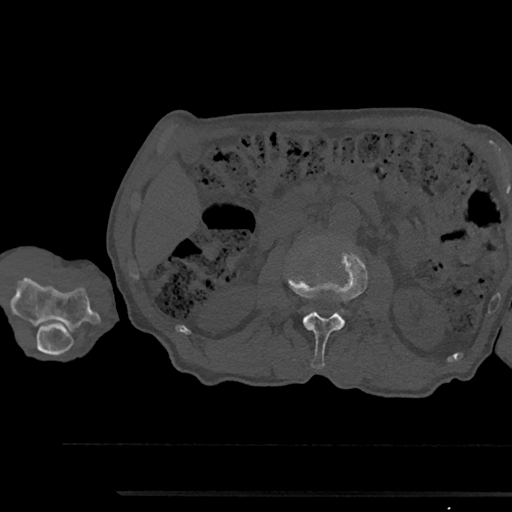
CT including the spine, one axial slice; position 547 of 797 along the scan axis; reconstruction kernel Br40s/3; bone window (W 1800 / L 400 HU); 0.5 mm slice thickness; 512 × 512 image matrix, field of view 367 × 367 mm. Patient: male, 79 years. From the clinical record (not read from this slice): primary cancer: prostate.
Structures marked on this image (semi-automatic segmentation, software-assisted and operator-edited):
- L2 vertebra: bounding box <287,246,367,368> (left, top, right, bottom; pixels)